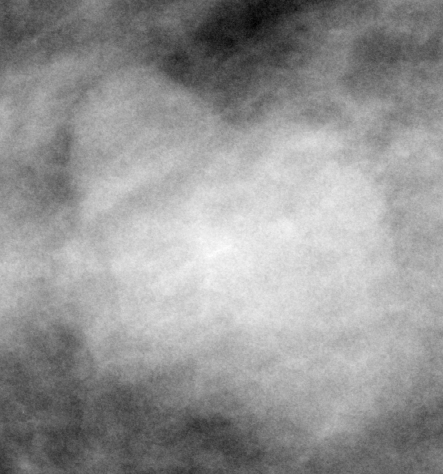
Region of interest cut from a scanned film mammogram (one marked finding); right breast; CC view; BI-RADS breast density category 3 (scale 1–4).
- Mass, shape lobulated, margins circumscribed; BI-RADS assessment category 4; pathology result (as recorded, not read from the image): benign.